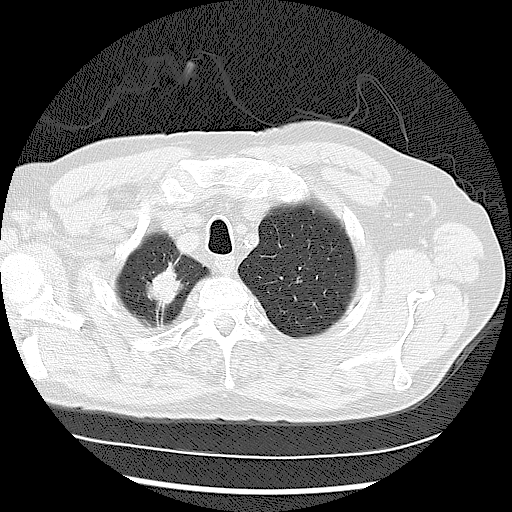
Low-dose screening chest CT, one axial slice; slice 103 of 122 in the series (ordered by position); reconstruction kernel LUNG; lung window (W 1500 / L -600 HU); 512 × 512 image matrix.
Annotated regions visible in this slice (outlined manually by an expert reader):
- lesion 2 (tumor, upper lobe of right lung): bounding box <146,263,183,308> (left, top, right, bottom; pixels)